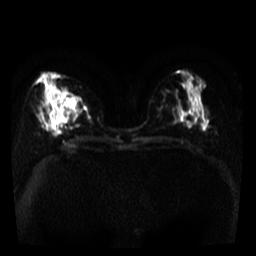
Breast MRI, one axial slice. Slice 18 of 39 in the series (ordered by position). Diffusion-weighted series; image 2 of 4 stored at this slice position (different b-values; order by instance number). 3 T. 256 × 256 image matrix, field of view 280 × 280 mm. Female patient.
Annotated regions visible in this slice (manually delineated by an expert):
- tumour on diffusion-weighted imaging: box from (x=60, y=95) to (x=80, y=112) px